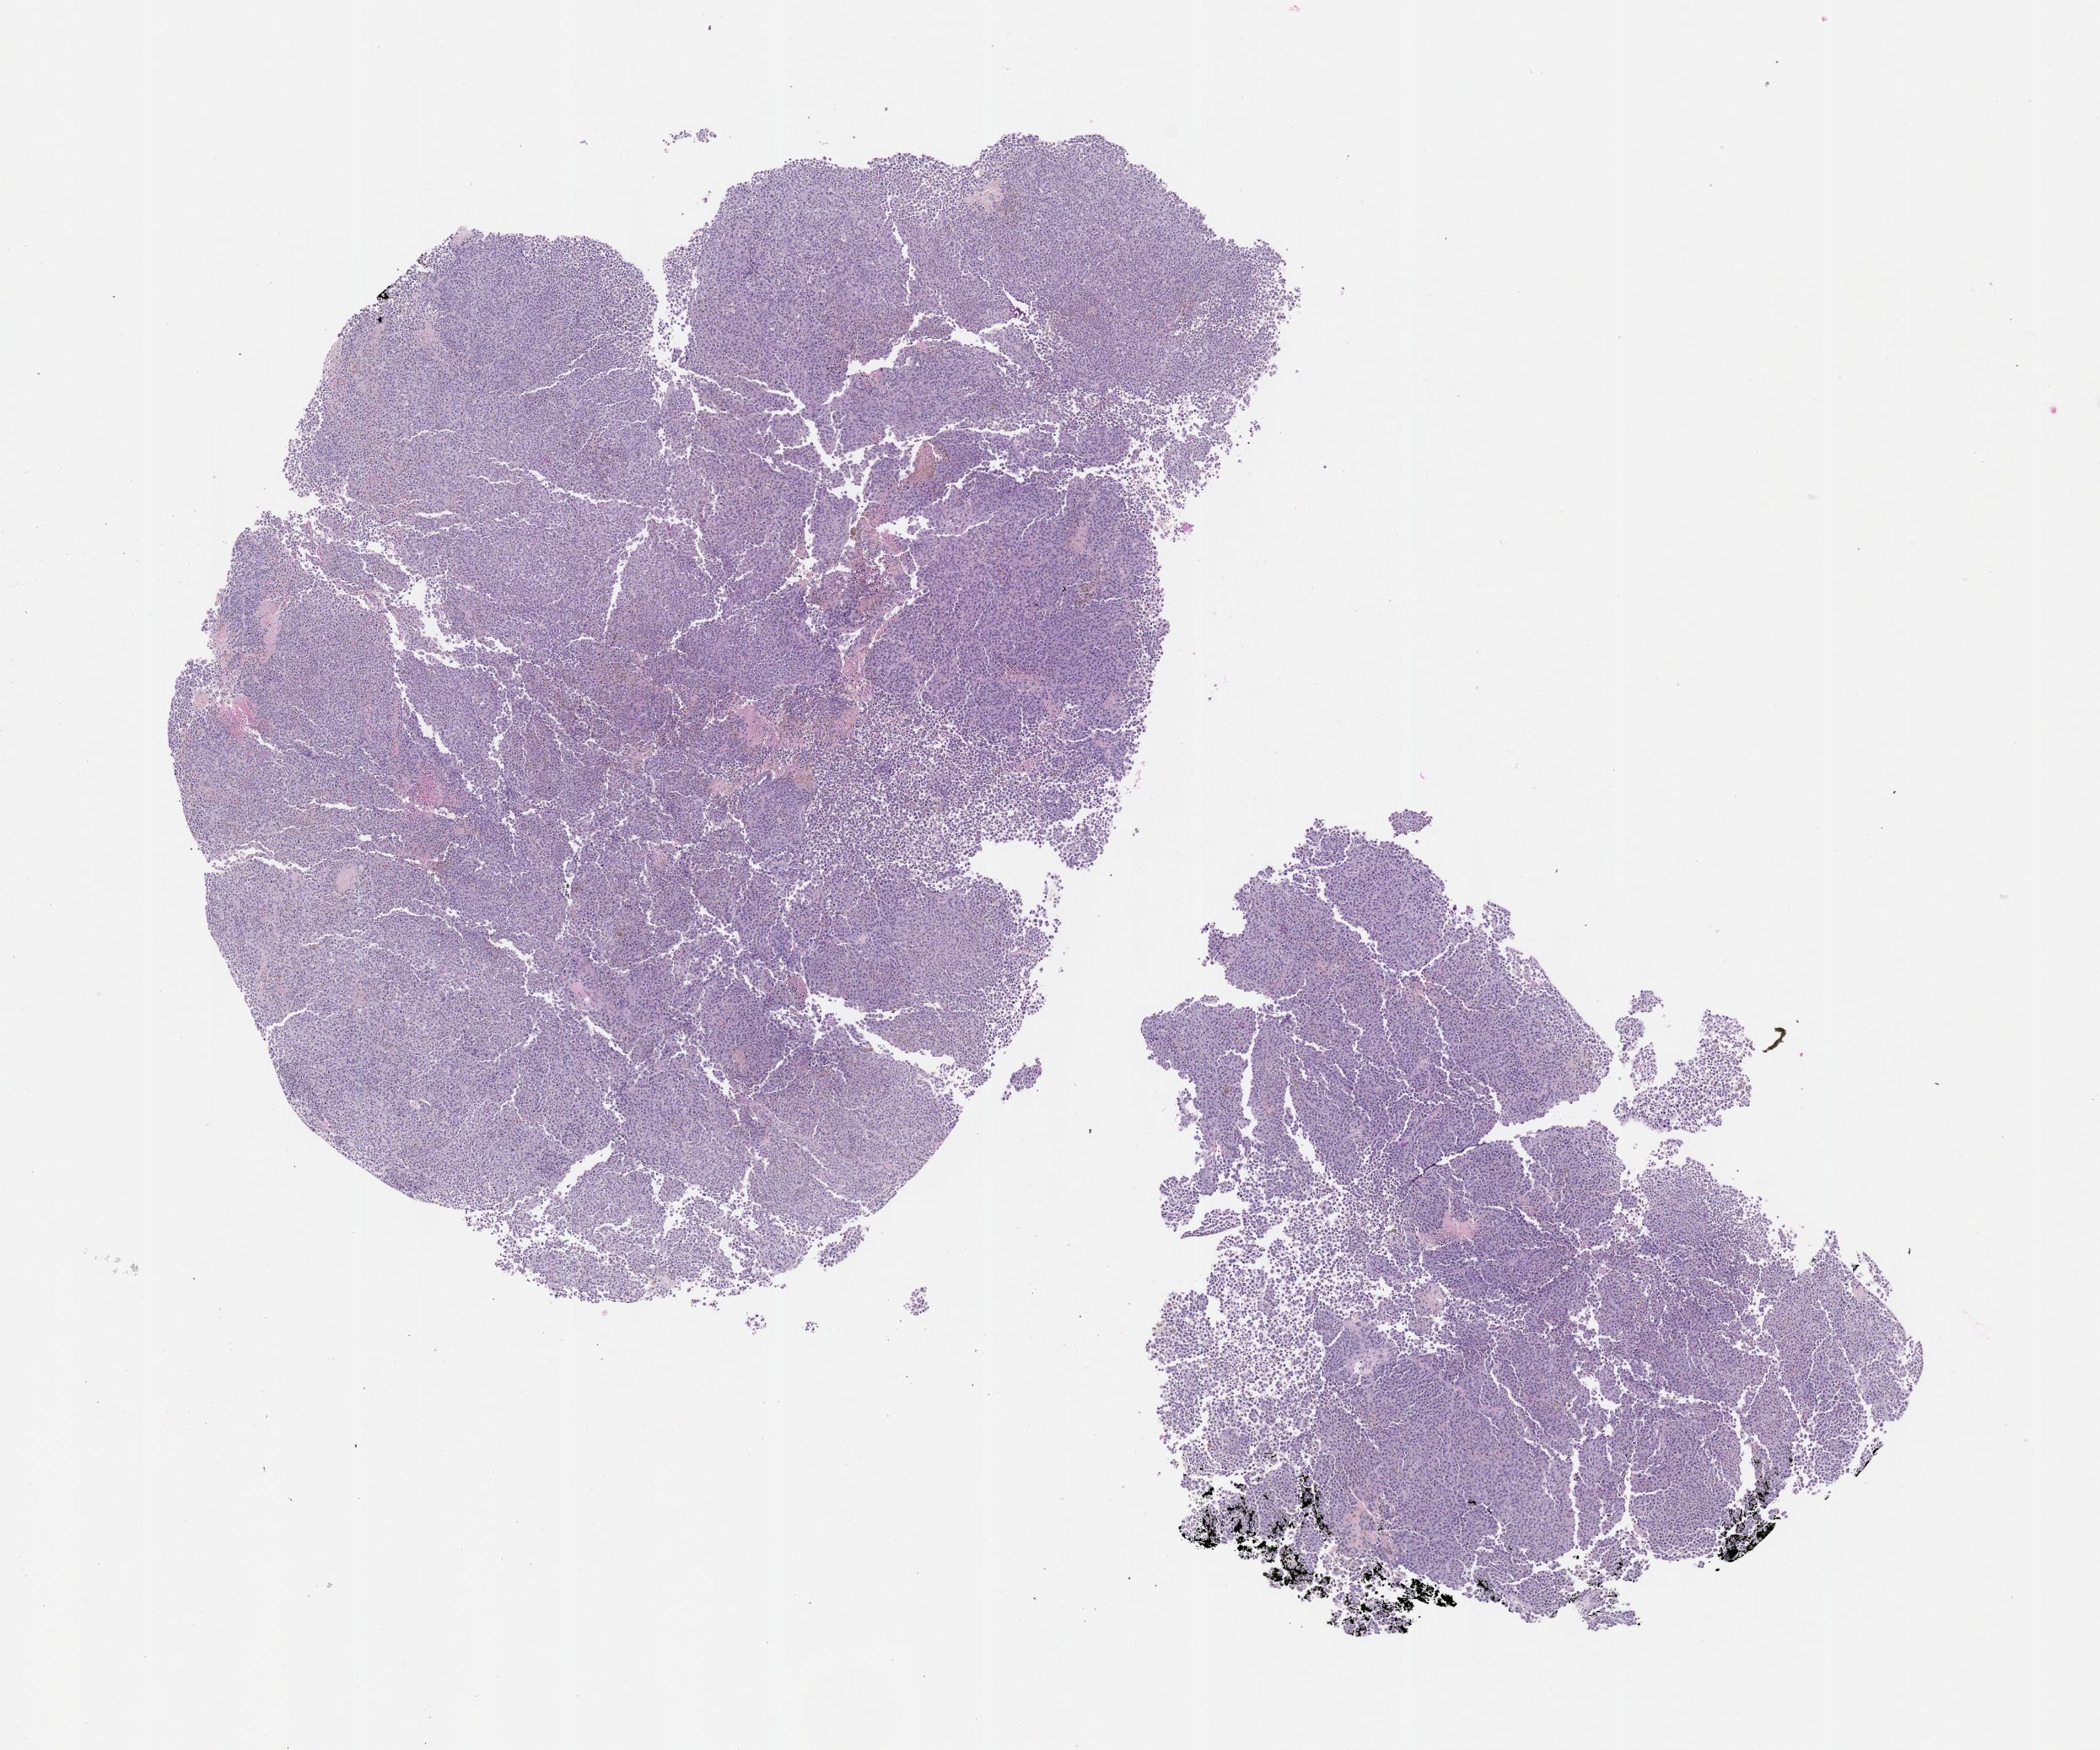
Hematoxylin and eosin (H&E) whole-slide image of a patient-derived xenograft (PDX) tumor grown in a mouse, passage 1 — shown as a low-resolution overview of the whole scanned area (about 10.0 x 8.3 mm); formalin-fixed paraffin-embedded section; tumor site category: skin.
* originating patient diagnosis: Melanoma